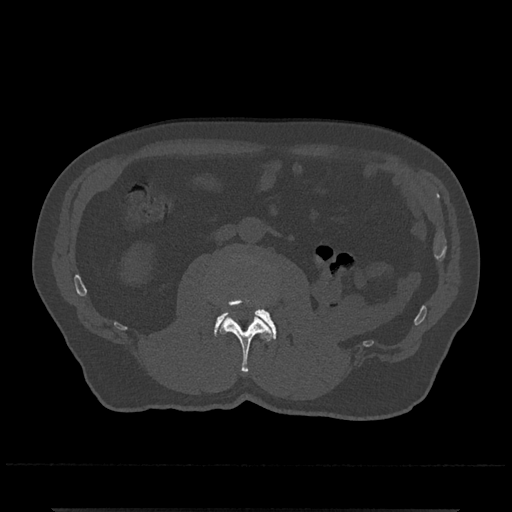
CT including the spine, one axial slice. Position 266 of 797 along the scan axis. 120 kVp. Bone window (W 1800 / L 400 HU). 0.5 mm slice thickness. 512 × 512 image matrix, field of view 393 × 393 mm. Patient: male, 67 years. From the clinical record (not read from this slice): primary cancer: prostate.
Structures marked on this image (semi-automatic segmentation, software-assisted and operator-edited):
- L2 vertebra: bounding box (x1, y1, x2, y2) in pixels: (220, 299, 271, 373)
- L3 vertebra: (214, 257, 277, 339)